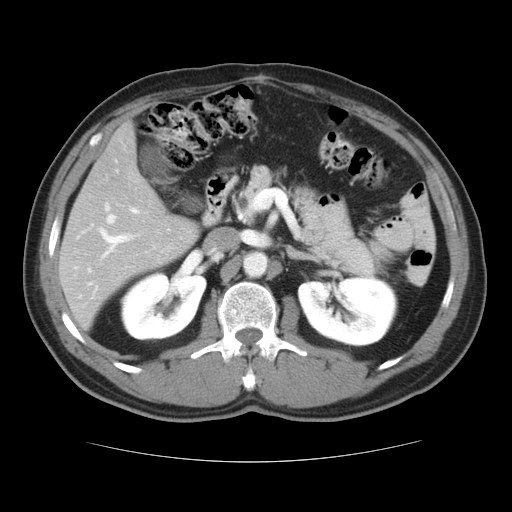
Contrast-enhanced abdominal CT, one axial slice; position 18 of 37 along the scan axis; intravenous contrast given; soft-tissue window (W 400 / L 40 HU); 5 mm slice thickness; 512 × 512 image matrix, field of view 374 × 374 mm. Male patient, age 66 years. Case-level facts recorded for this patient, not image findings: diagnosis: colorectal cancer liver metastases, imaged before liver resection; multiple liver metastases: yes; largest metastasis: 1.6 cm.
Outlined on this slice (outlined manually by an expert reader):
- hepatic veins: box from (x=104, y=203) to (x=117, y=225) px
- liver: (x=60, y=125)–(x=198, y=329)
- planned liver remnant (the part of the liver to remain after resection): (x=60, y=201)–(x=198, y=329)
- portal vein (with intrahepatic branches): (x=100, y=208)–(x=139, y=256)